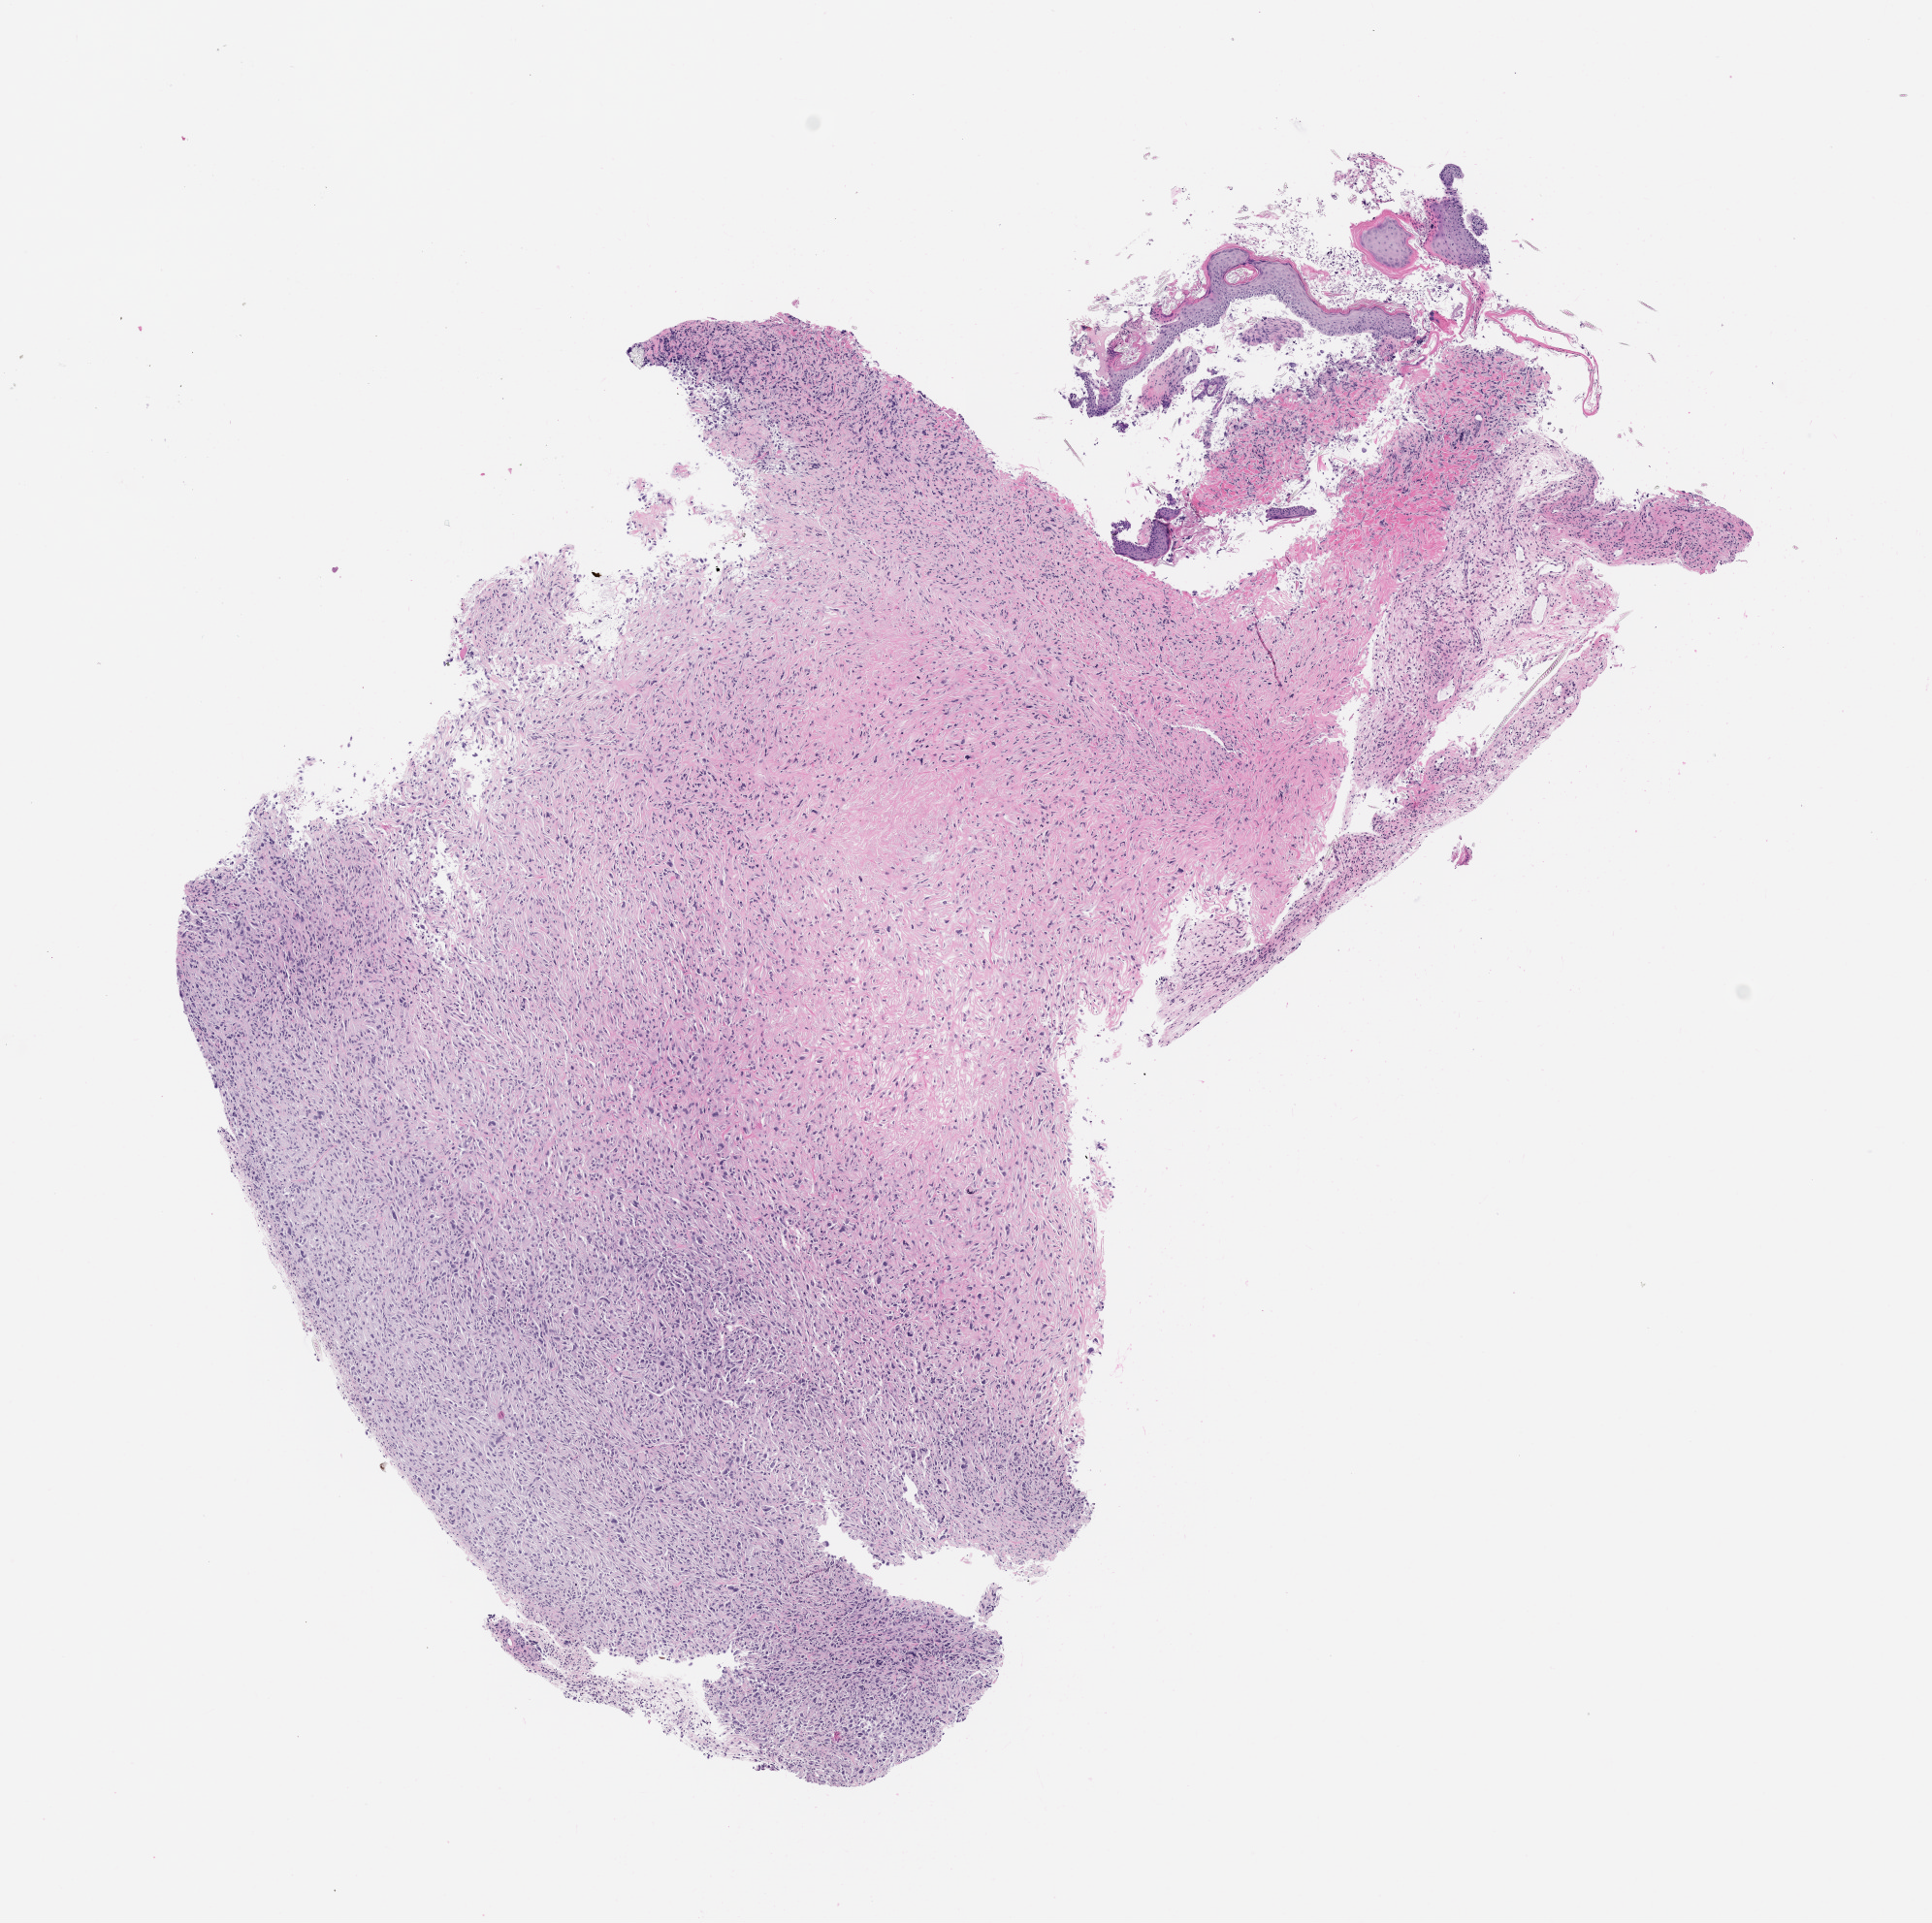
Haematoxylin and eosin whole-slide image of a patient-derived xenograft (PDX) tumor grown in a mouse, shown as a low-resolution overview of the whole scanned area (about 8.0 x 8.0 mm). Formalin-fixed, paraffin-embedded (FFPE) tissue. Originating tumor site category: musculoskeletal.
- originating patient diagnosis: Spindle Cell Sarcoma